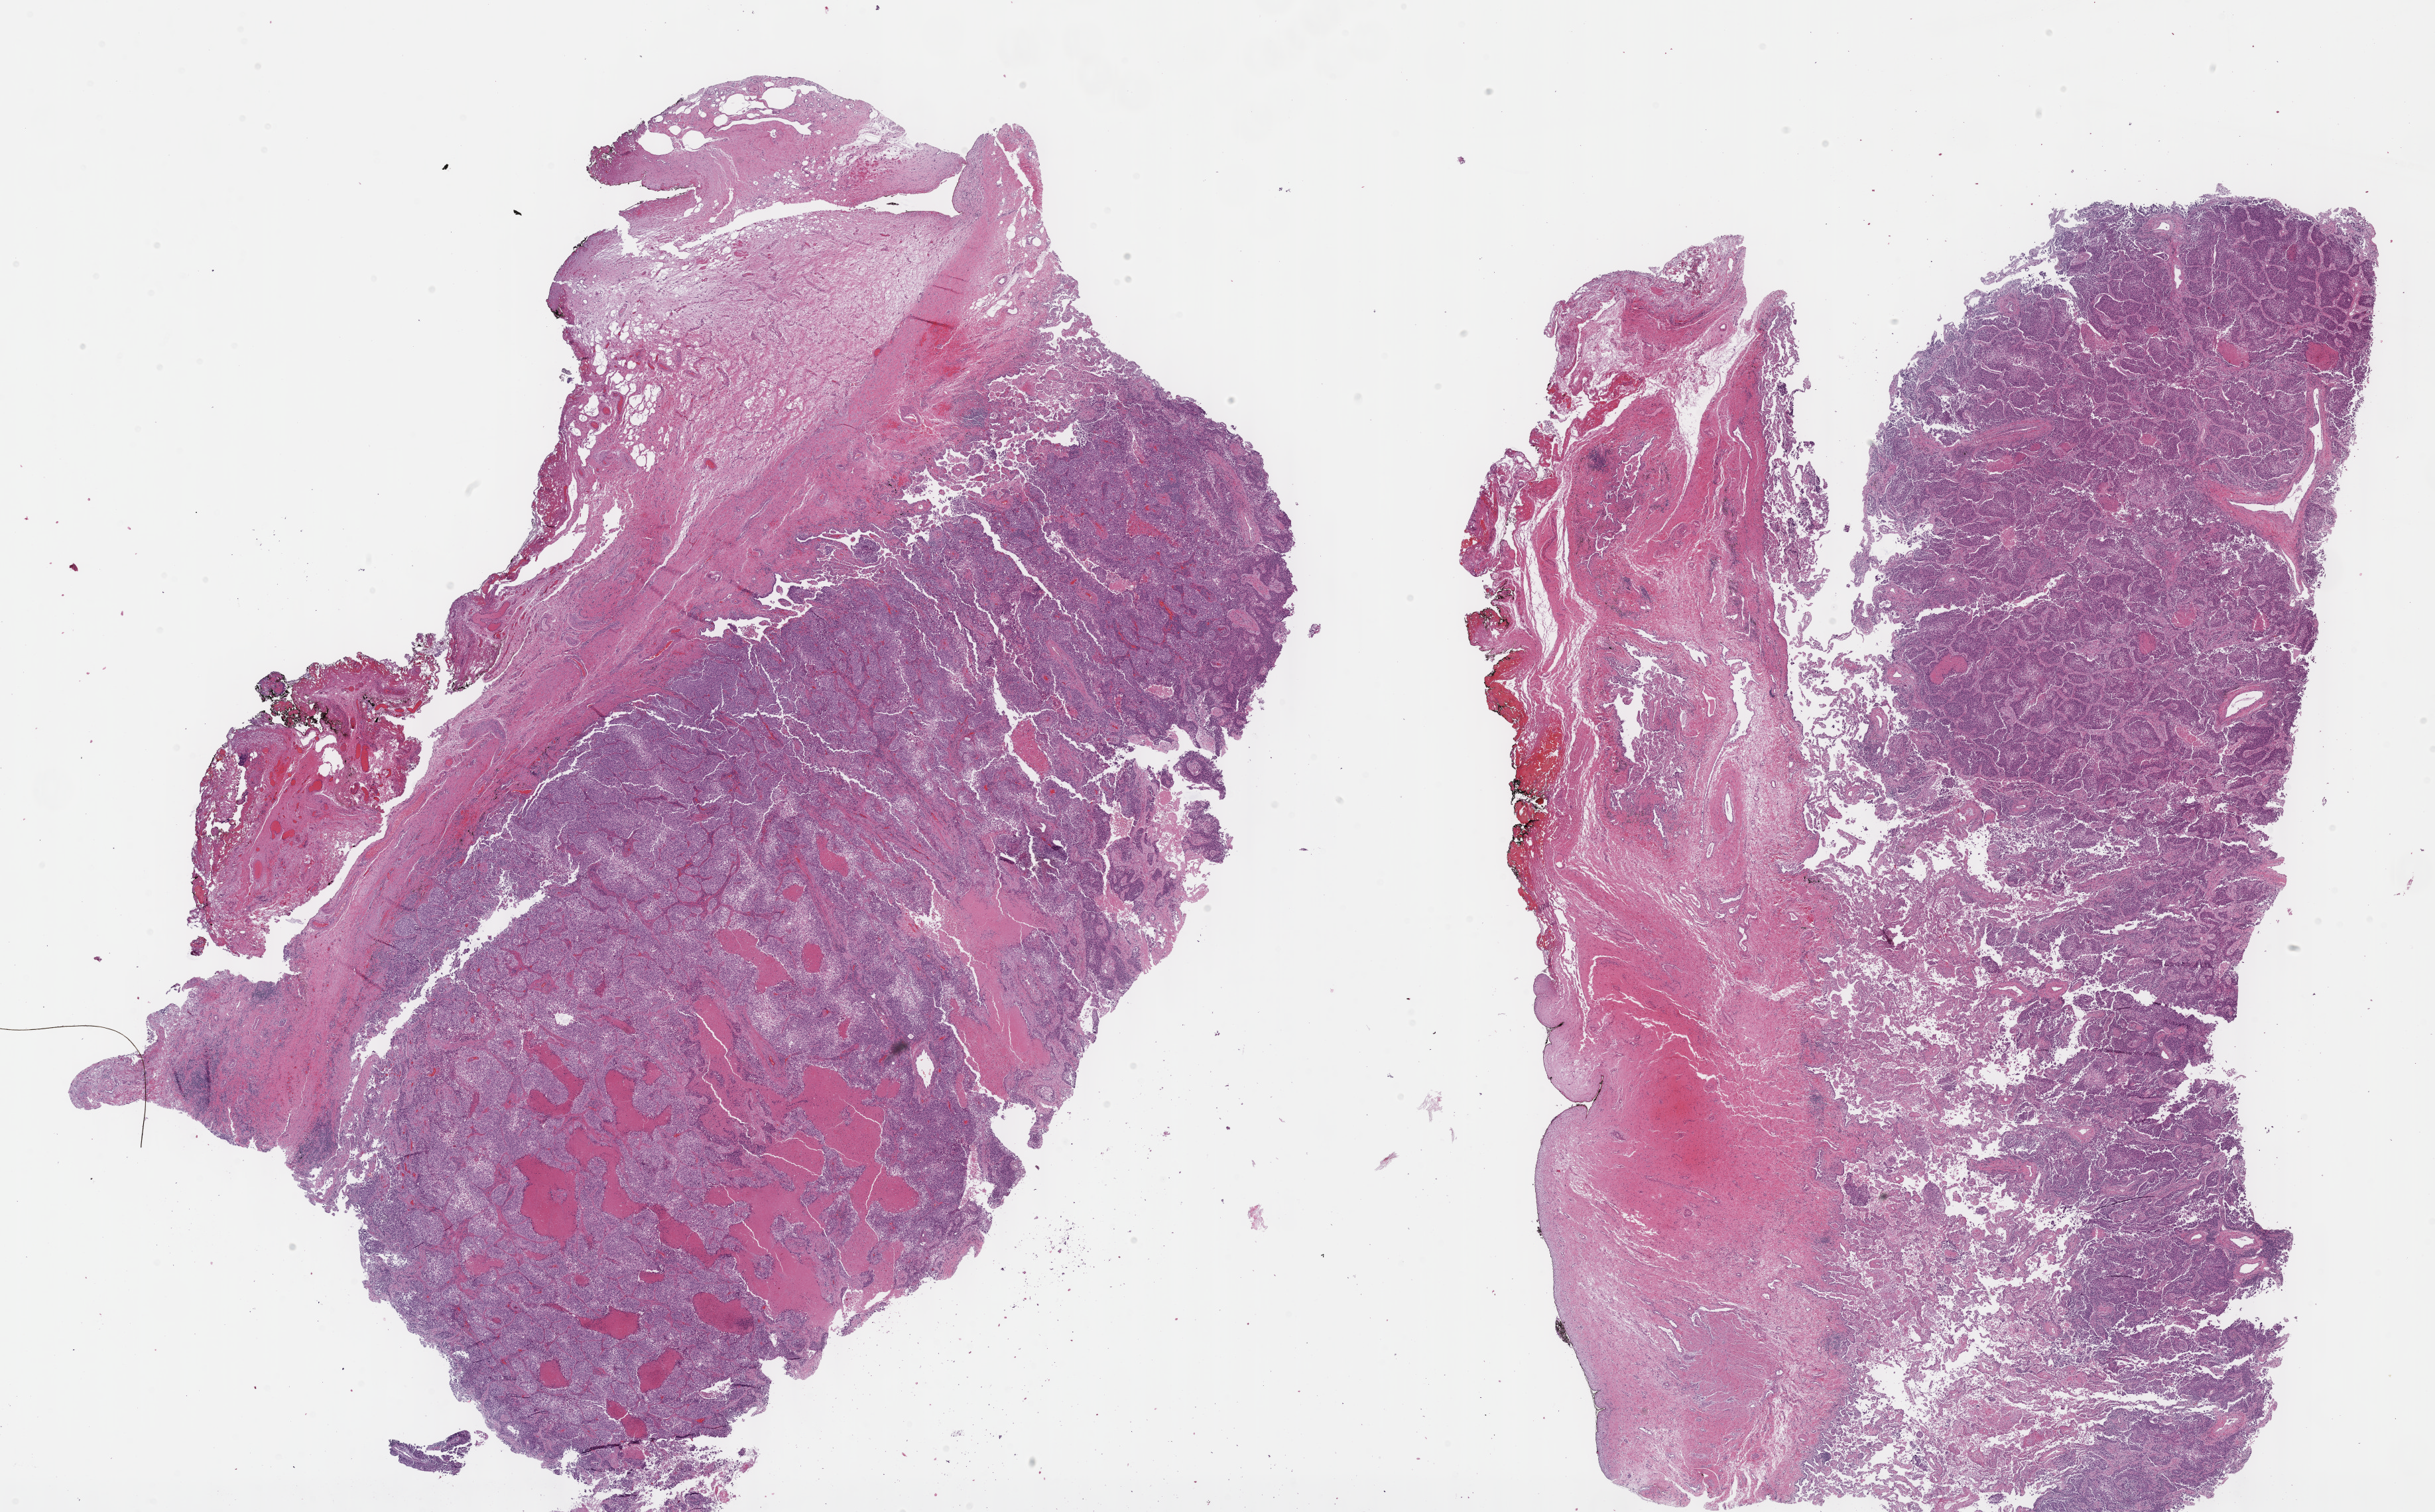
H&E whole-slide image — whole scanned area (about 29.7 x 18.4 mm, from a 40x scan) shown as a low-resolution overview; FFPE section; primary tumour sample from the lung. Male patient; age at initial diagnosis 70 years.
- histologic diagnosis: Squamous cell carcinoma, NOS (lower lobe, lung)
- AJCC pathologic stage: IIA (7th edition)